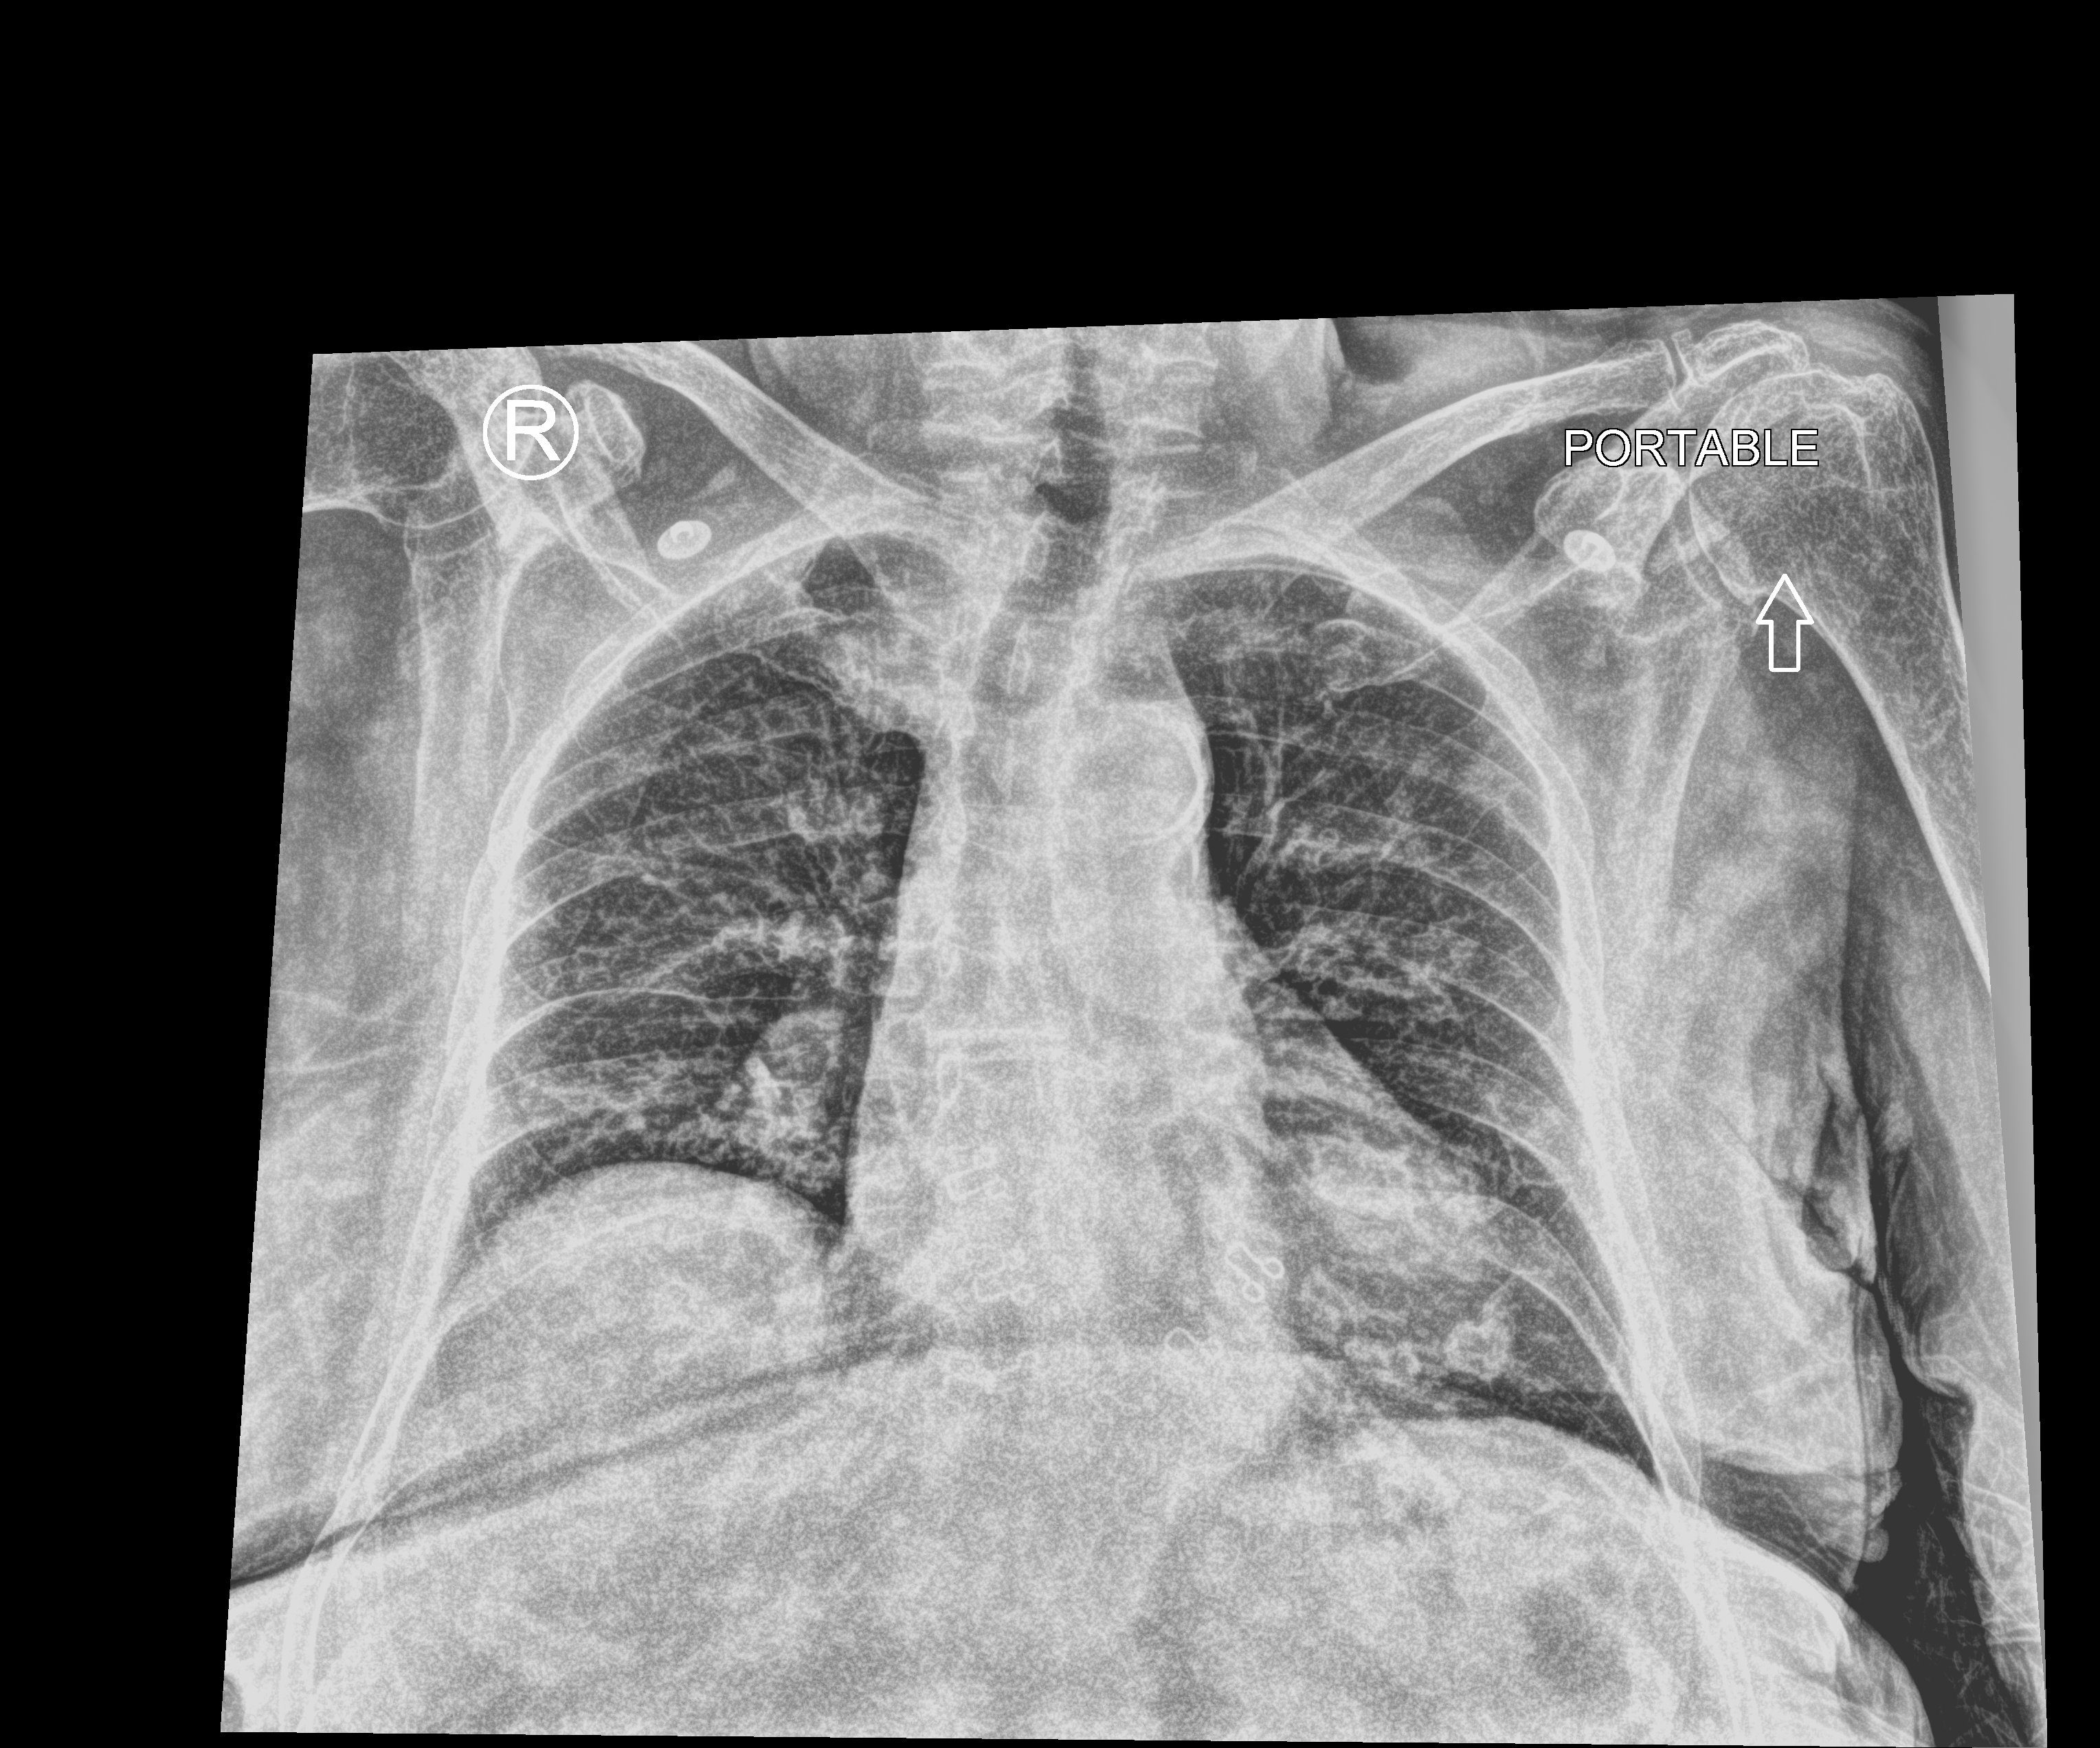
Bedside chest radiograph (computed radiography). Female patient hospitalised with COVID-19, age 75–90 years.
Hospital-stay facts (about this admission, not read from this image; timing relative to this image not recorded): length of hospital stay: 4 days; admitted to intensive care during this hospital stay: no; mechanically ventilated during this hospital stay: no.